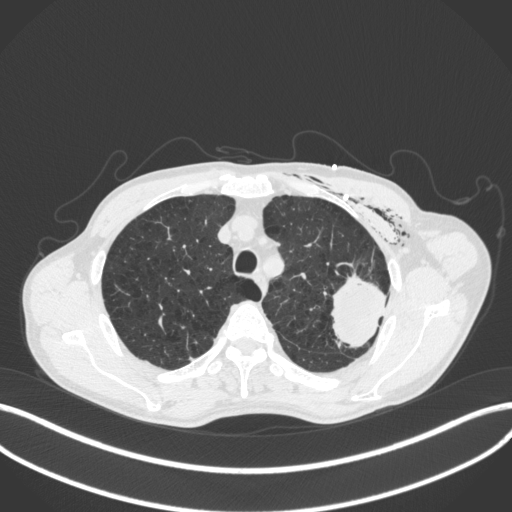
Chest CT, one axial slice. Slice 321 of 416 in the series (ordered by position). Reconstruction kernel B31f. Lung window (W 1500 / L -600 HU). 1 mm slice thickness. 512 × 512 image matrix, field of view 400 × 400 mm. Male patient, age 58 years. Case-level facts recorded for this patient, not image findings: clinical TNM (as recorded): T3 N0 M0.
Outlined on this slice (rectangle marked by the reading radiologist):
- lung tumour (recorded histology: adenocarcinoma): bounding box [x1, y1, x2, y2] px = [330, 273, 395, 352]